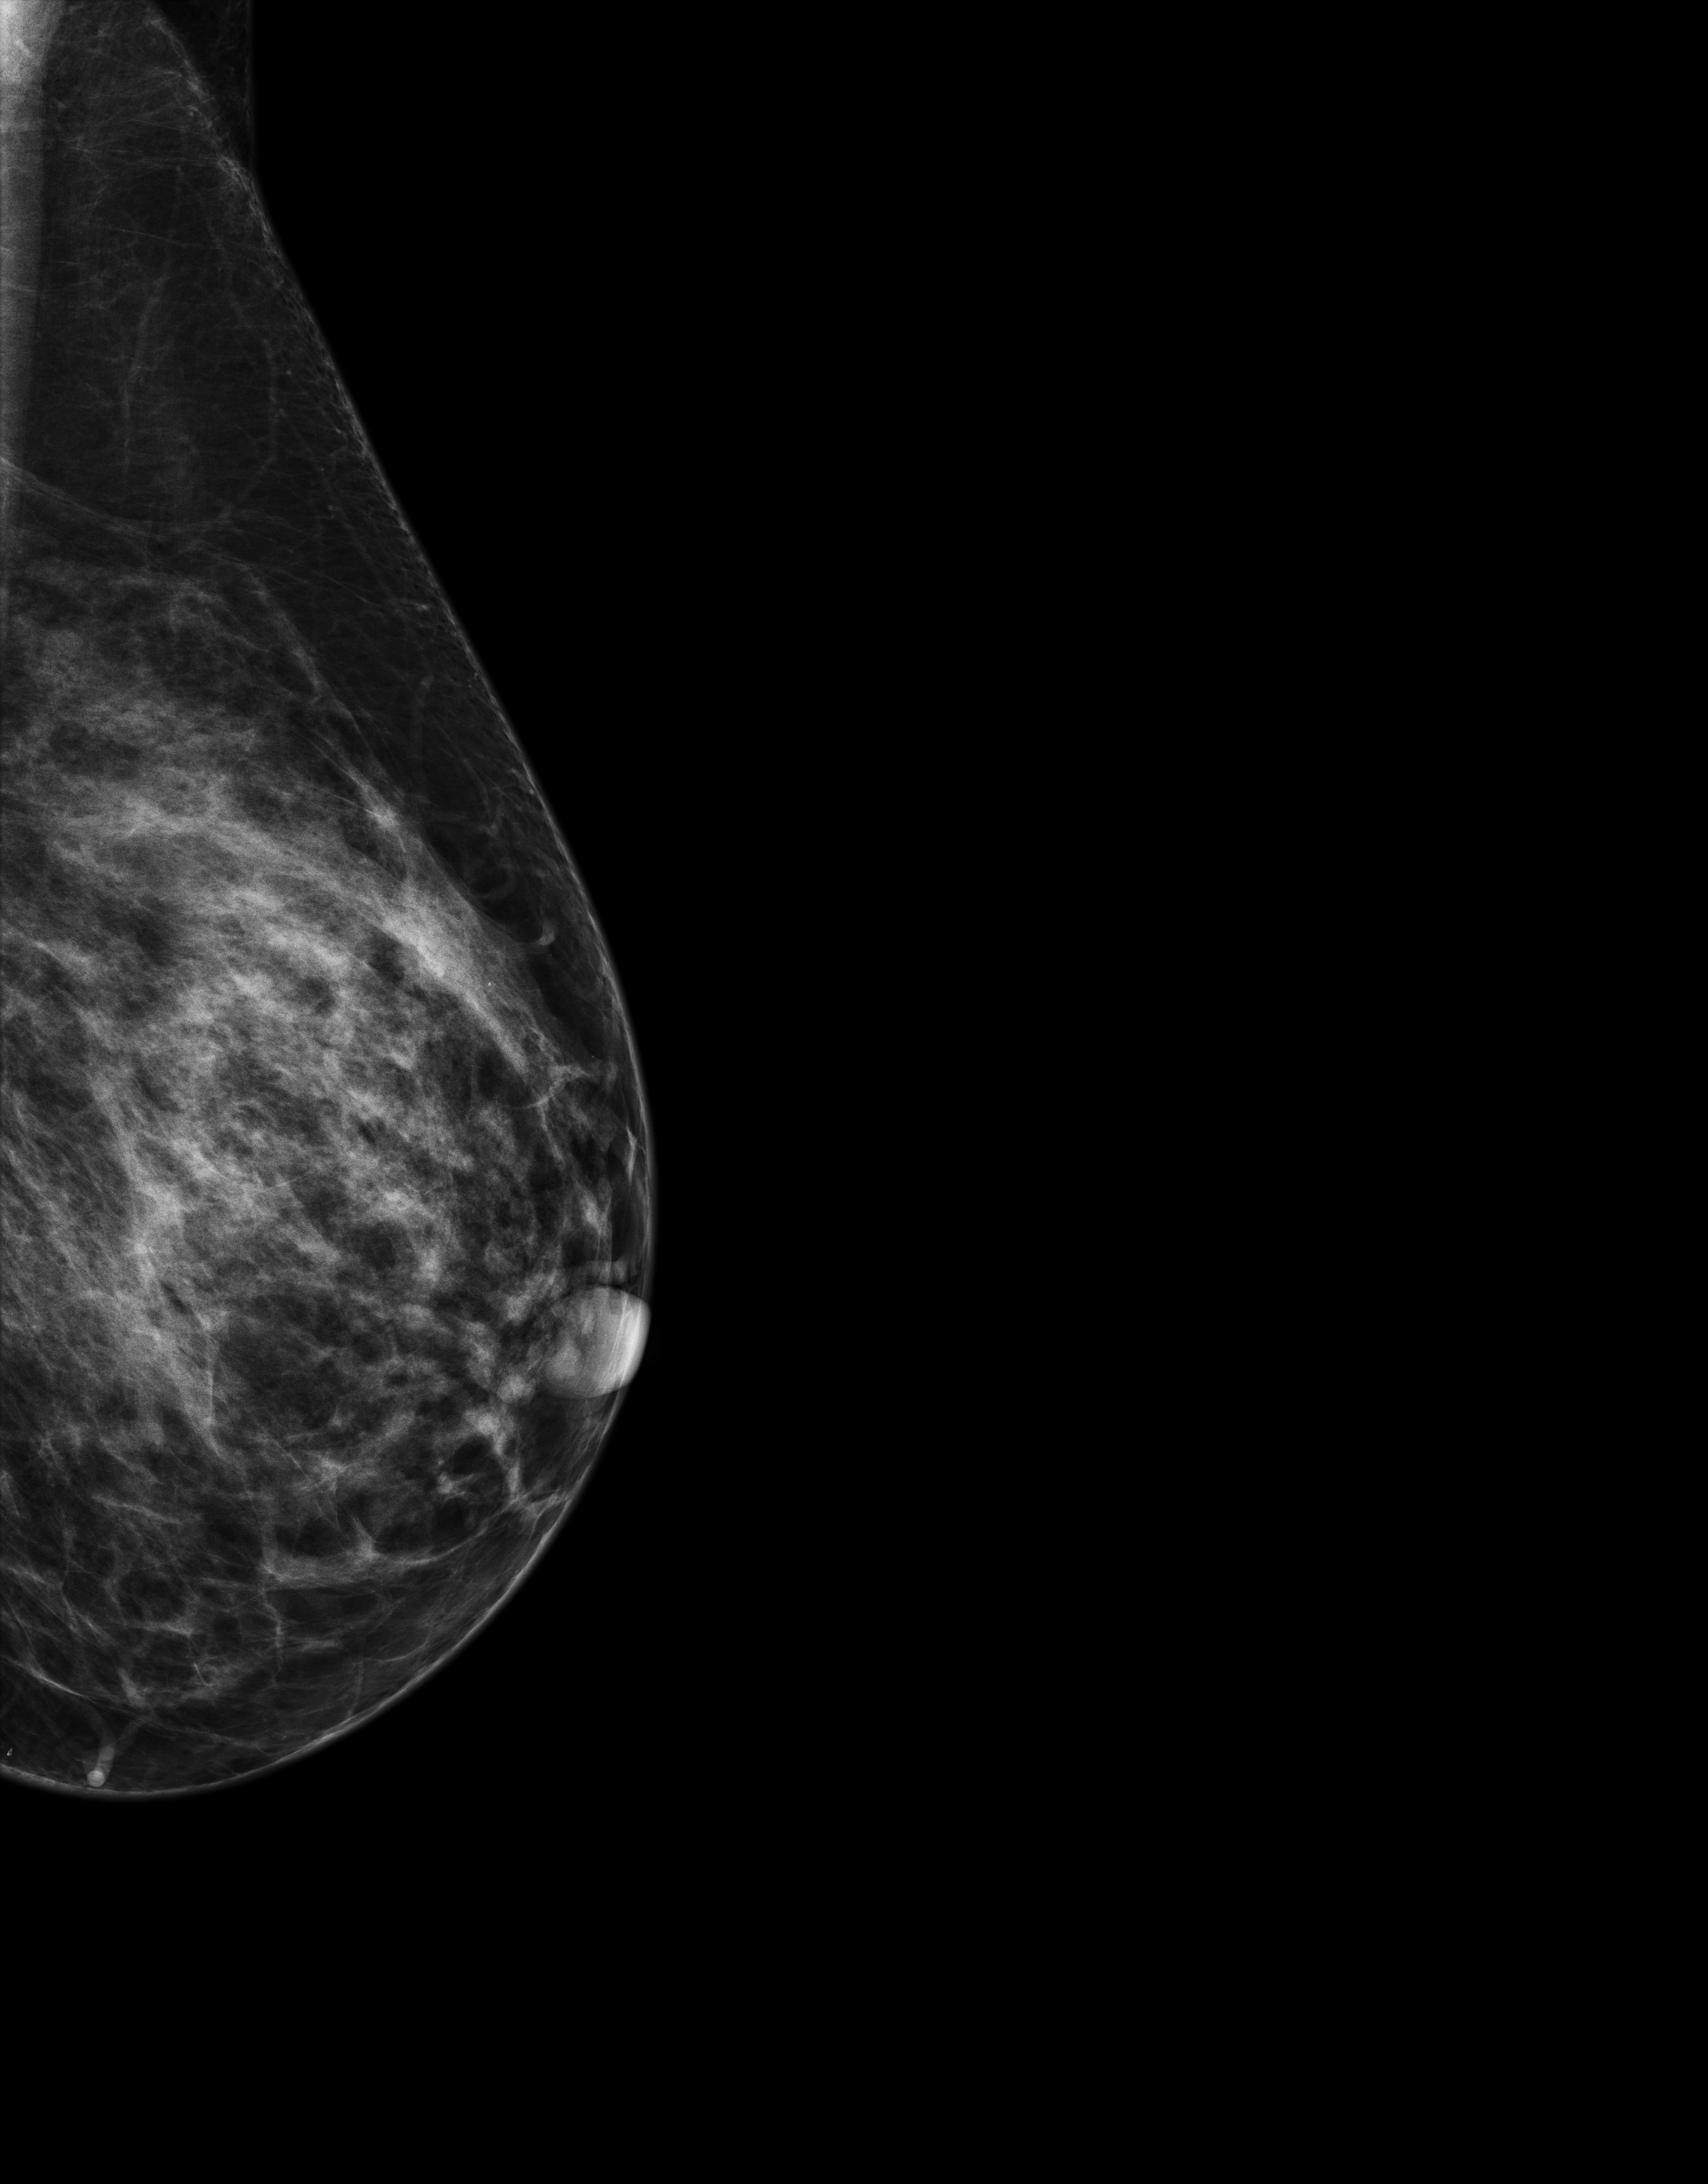
Full-field digital mammogram (FFDM), left breast, exaggerated CC view (lateral), screening examination, compressed breast thickness 69 mm. Patient aged 49 years (female).
- breast density at the screening exam (both breasts): heterogeneously dense (BI-RADS density category c)
- final BI-RADS assessment for this screening round (tomosynthesis exam, both breasts): category 1
- recall: no recall after this screen